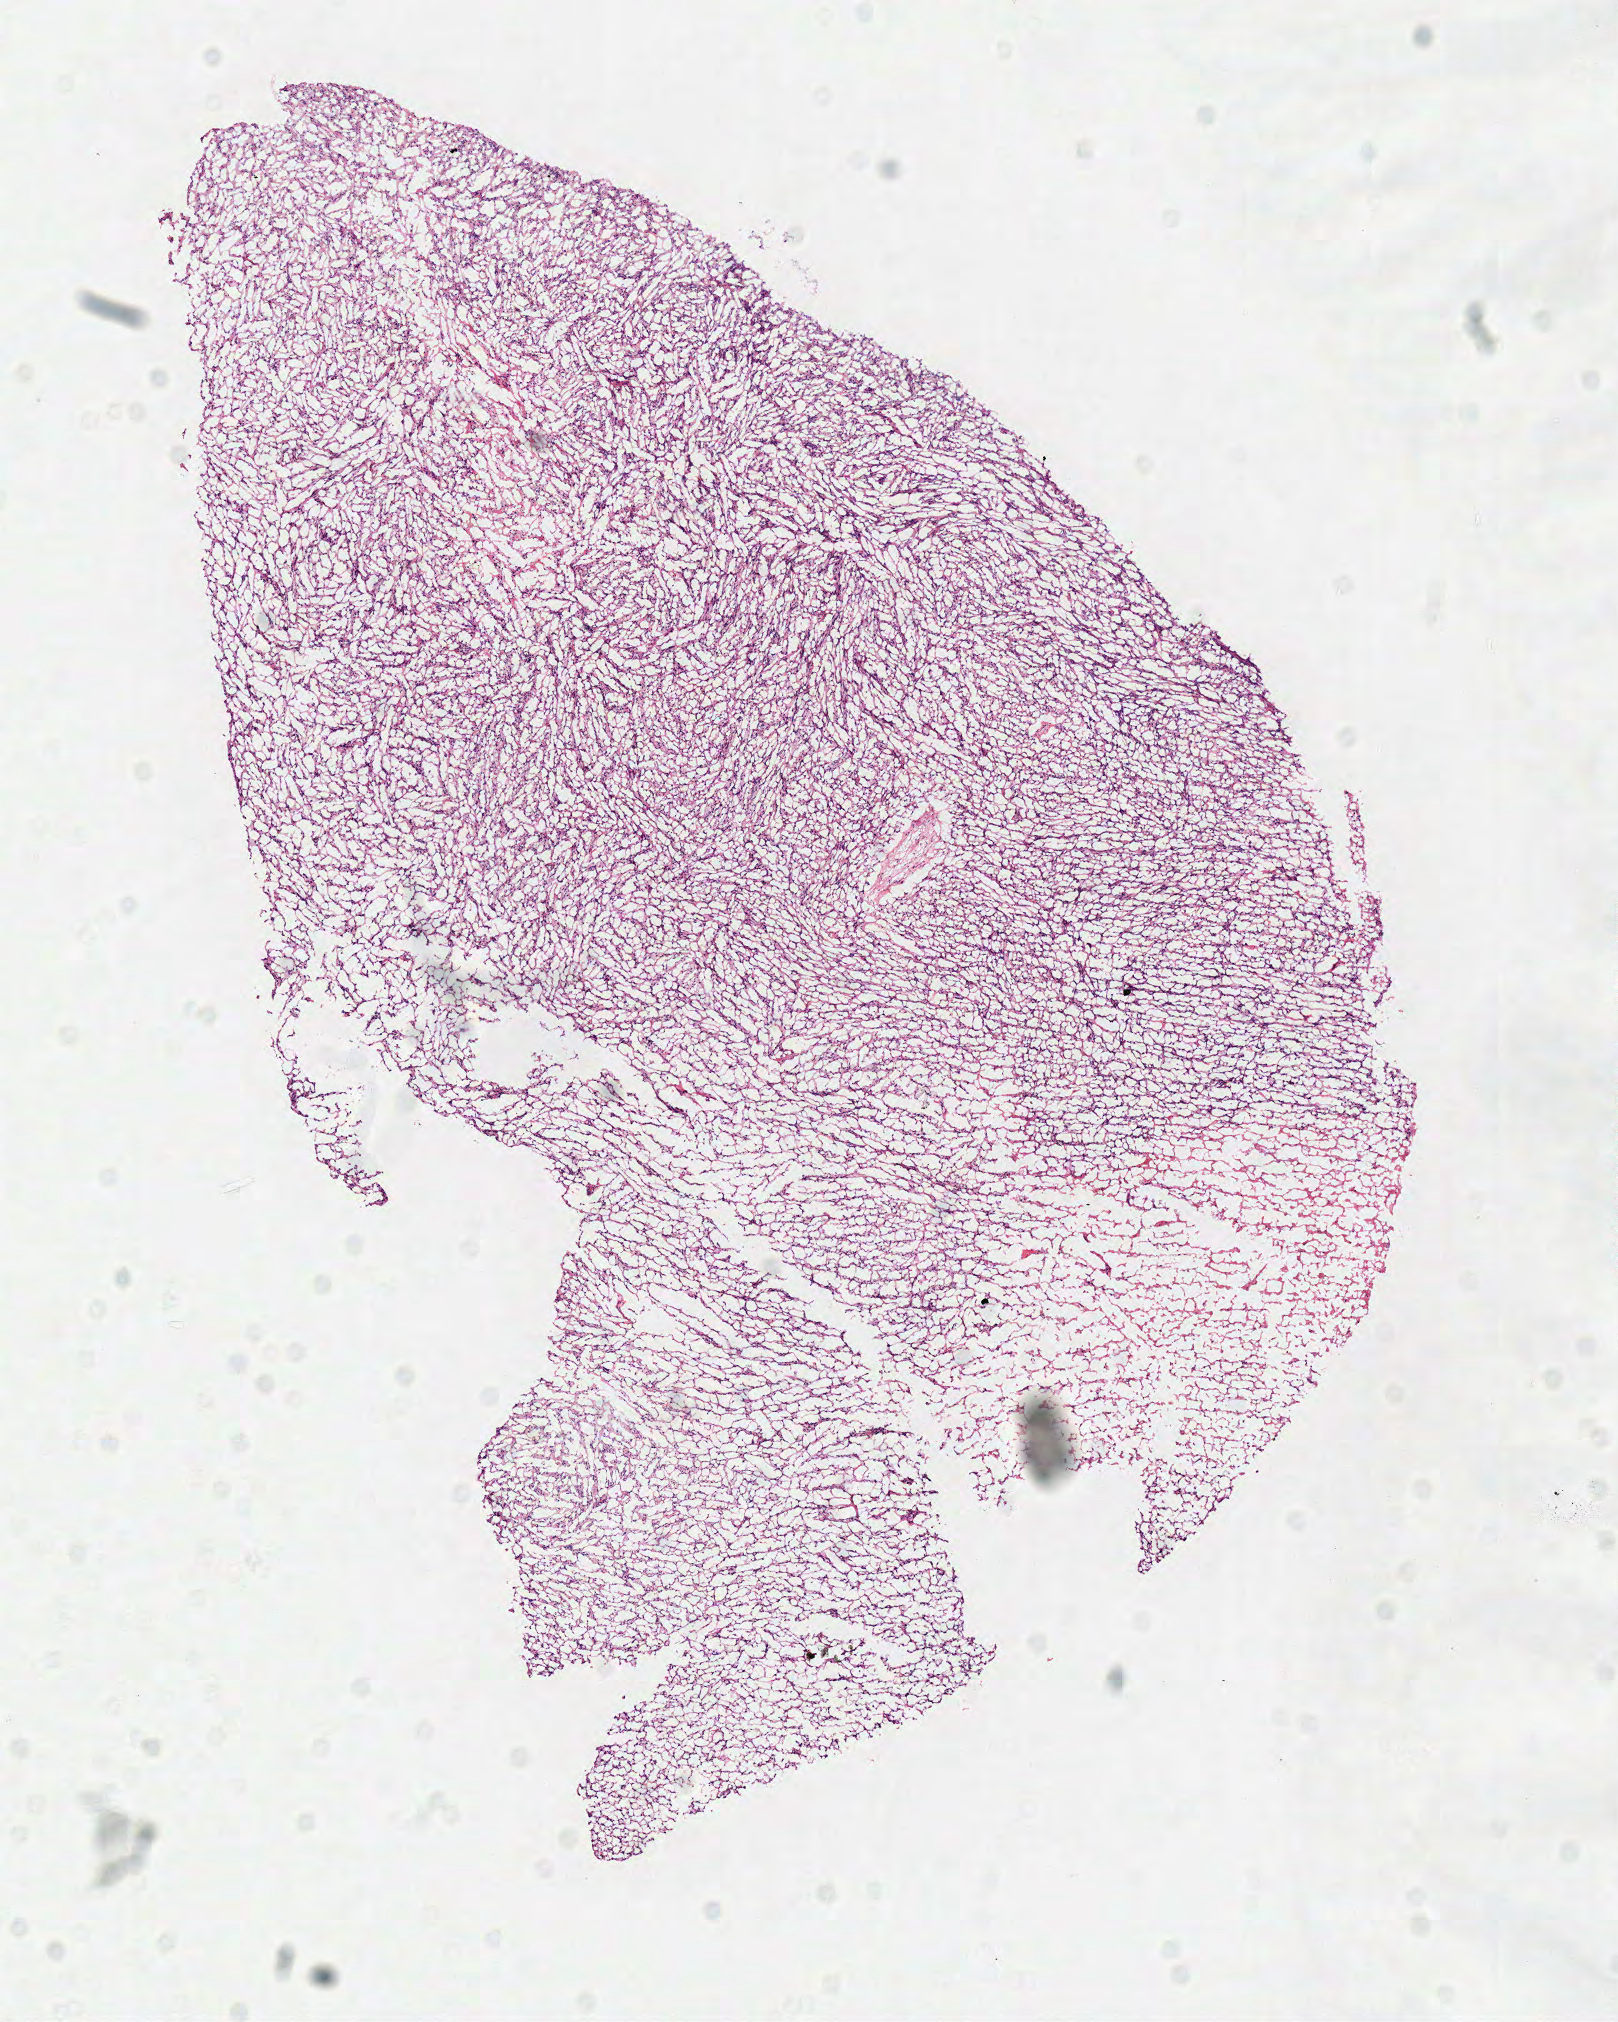
Whole-slide histology image, H&E, shown as a low-resolution overview of the whole scanned area (about 6.4 x 8.0 mm). Frozen section from the top of the tissue portion. Primary tumour sample from the brain. Female patient; age at initial diagnosis 76 years.
Diagnosis: Glioblastoma.